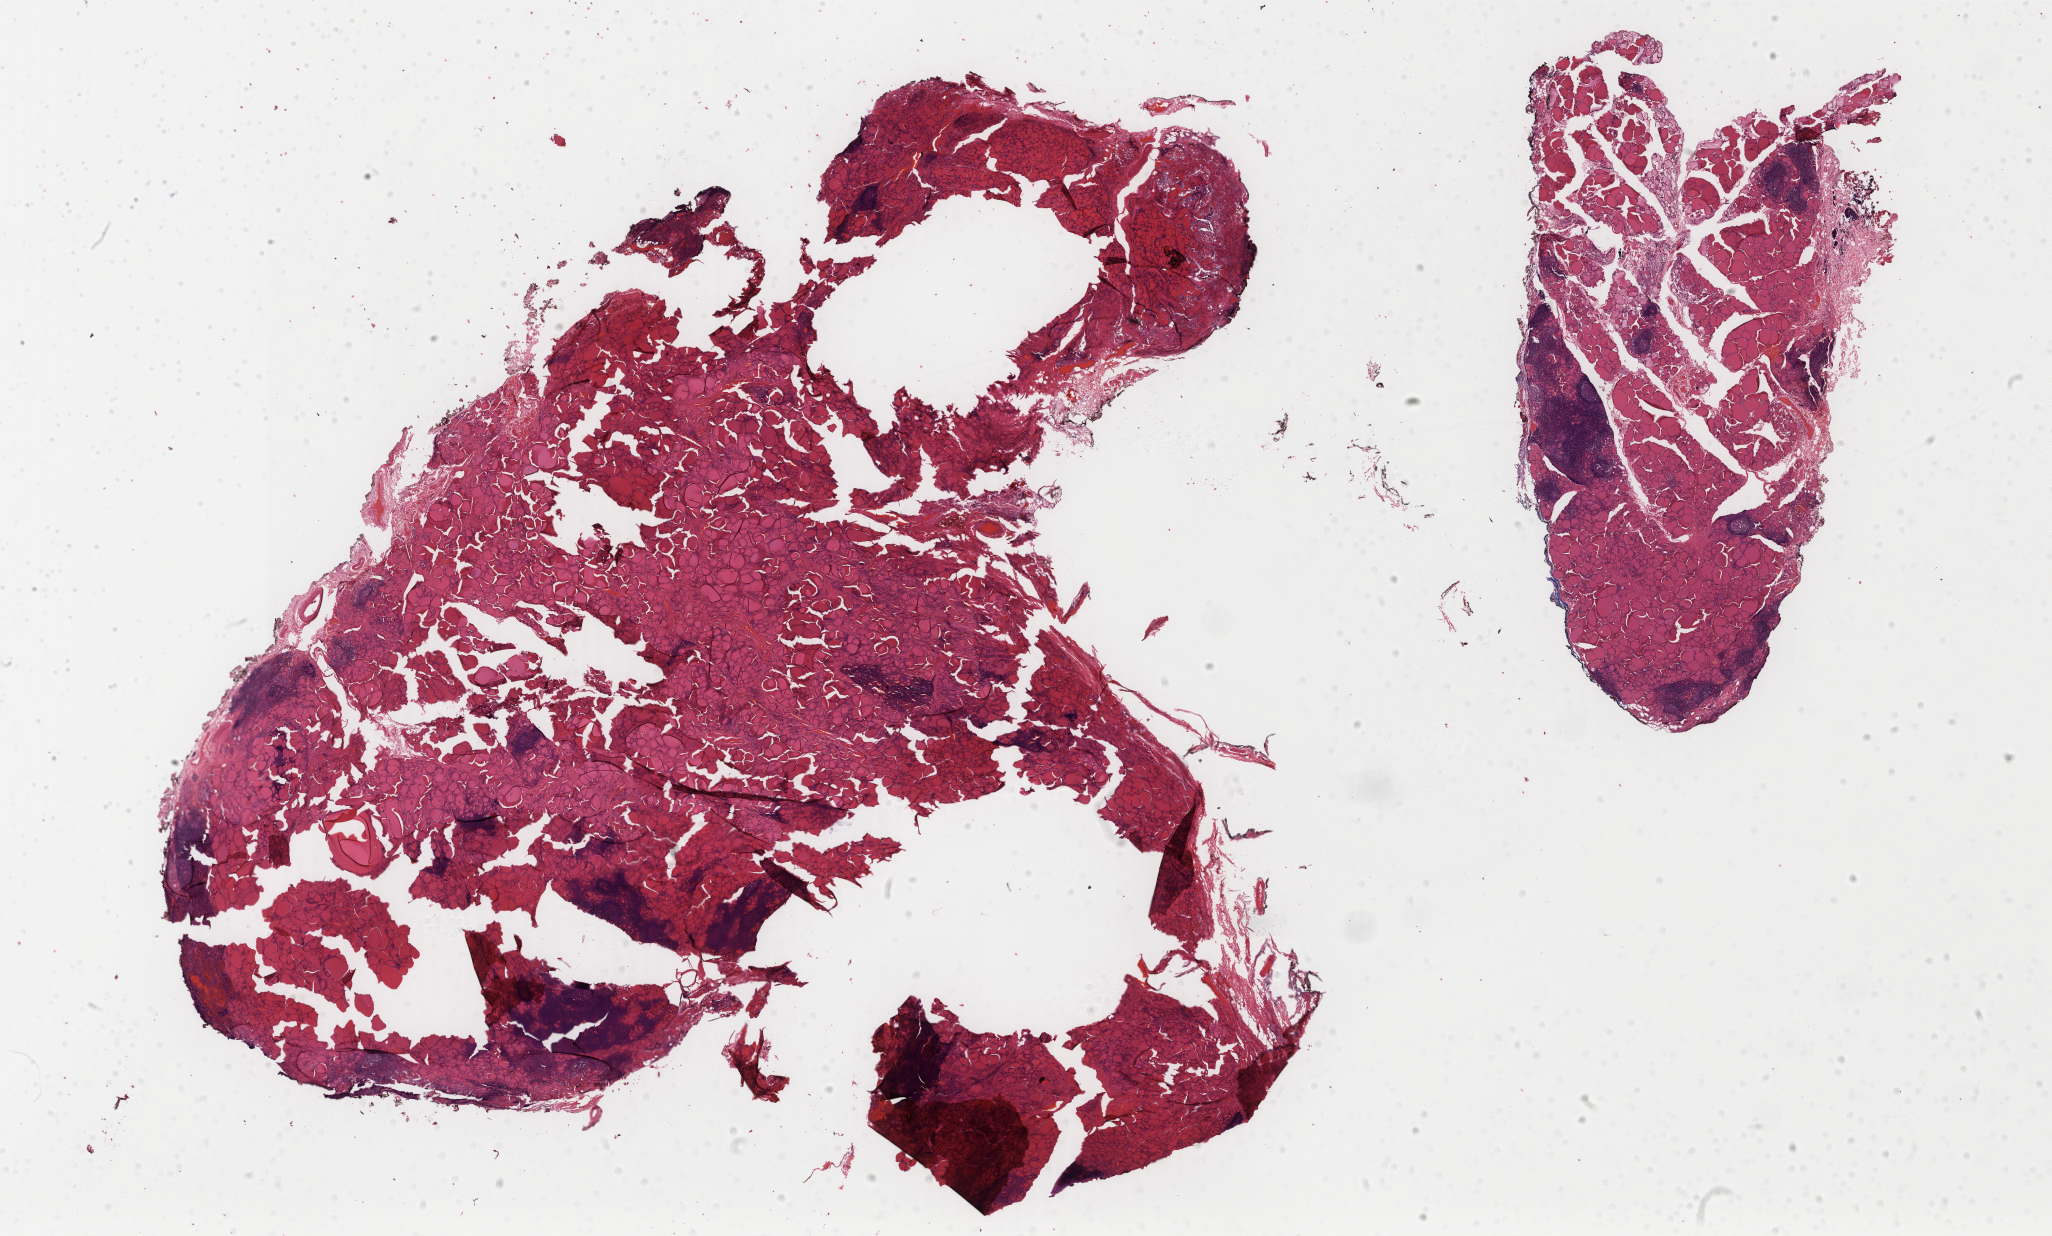
H&E whole-slide image, low-resolution overview of the scanned area, about 32.6 x 19.6 mm (from a 40x scan), formalin-fixed paraffin-embedded (FFPE) diagnostic section, thyroid, primary tumour sample. Female, age 33 years at initial diagnosis.
Laterality: left. Histologic diagnosis: Papillary adenocarcinoma, NOS (thyroid gland). Lymph nodes positive (case pathology): 0 of 3 examined. TNM: T1 N0 M0. AJCC pathologic stage: I.